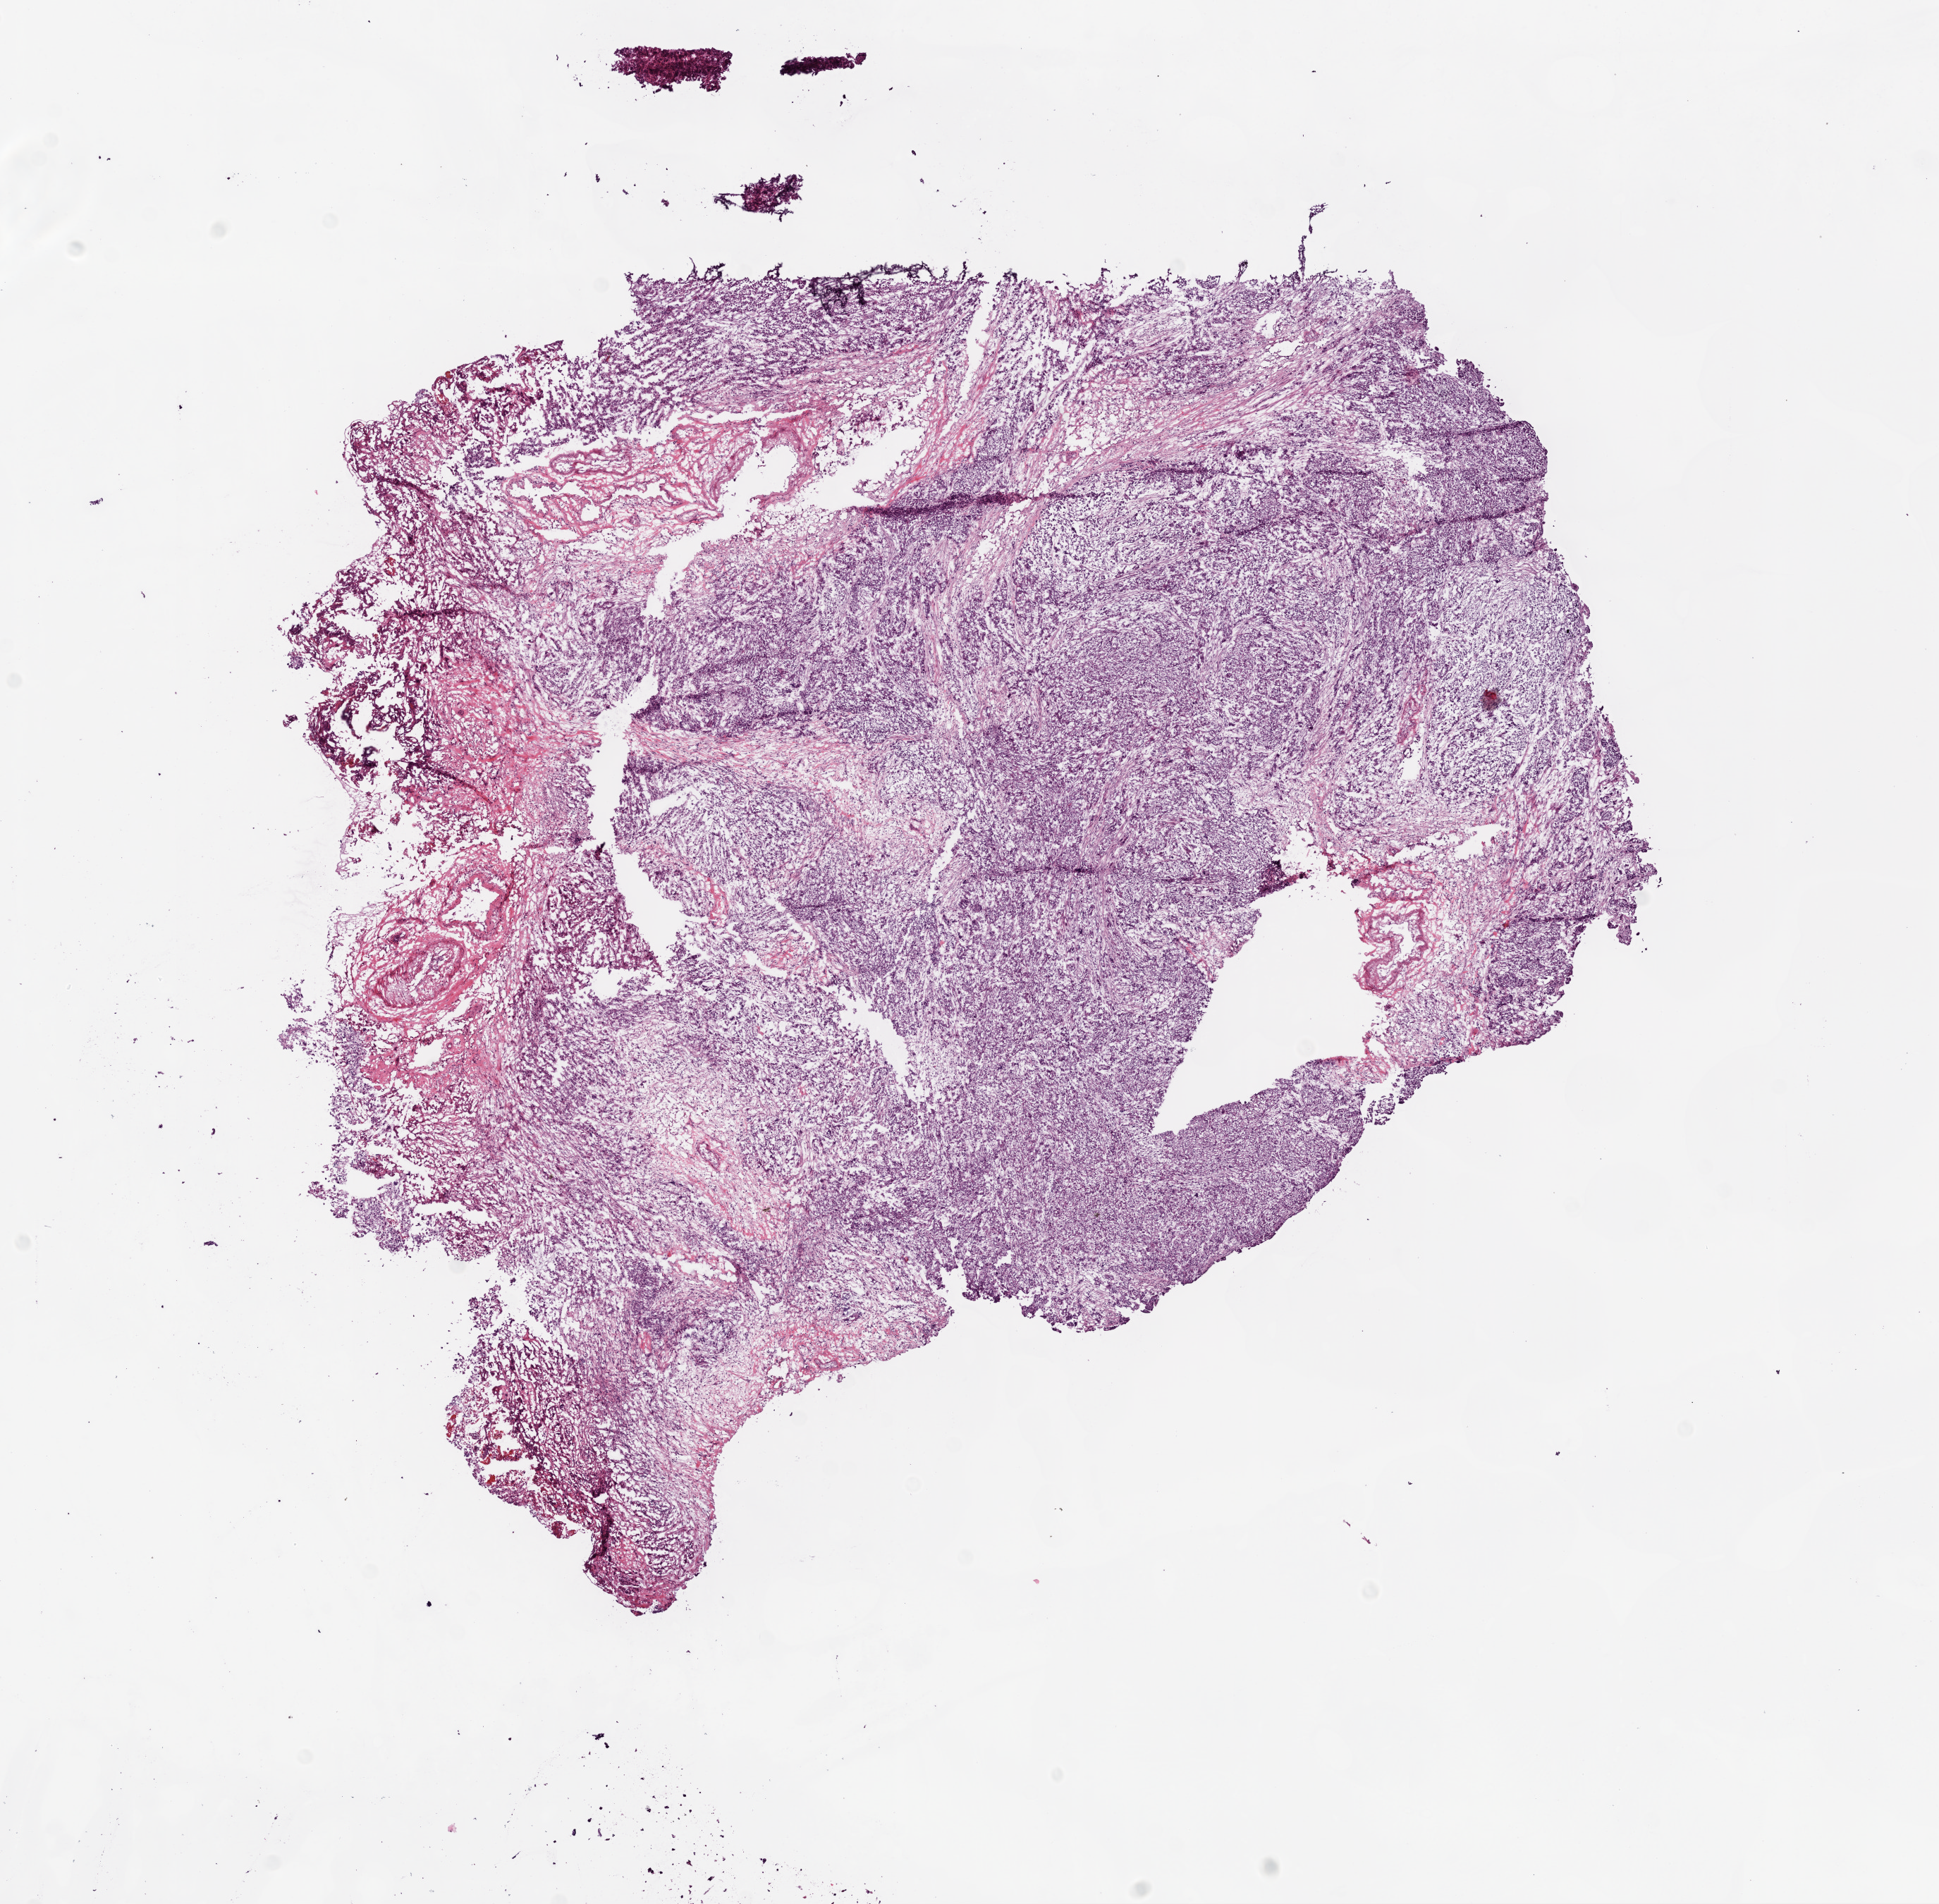
H&E whole-slide image — whole scanned area (about 11.0 x 10.8 mm) shown as a low-resolution overview. Frozen section. Sample: primary tumour, ovary. Female, age 64 years at initial diagnosis. Histologic grade: G3 (poorly differentiated). Slide review estimates, as recorded: tumour cells 80%, tumour nuclei 90%, normal cells 0%, stromal cells 20%, necrosis 0%.
Pathologic diagnosis: Serous cystadenocarcinoma, NOS. Laterality: right. FIGO stage: IV.